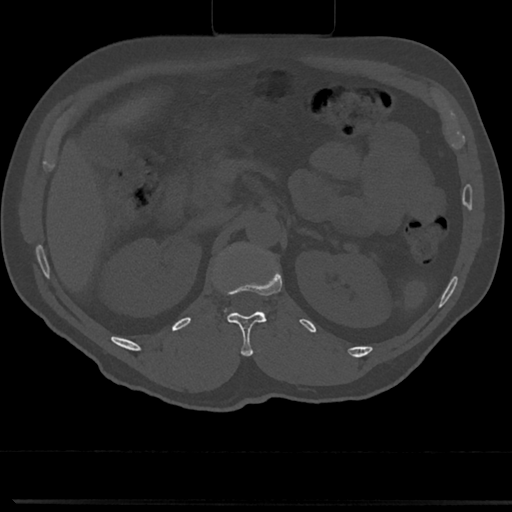
CT including the spine, one axial slice; reconstruction kernel Br40s/3; 120 kVp; bone window (W 1800 / L 400 HU); 512 × 512 image matrix. Patient: male, 61 years. From the clinical record (not read from this slice): primary cancer: prostate.
Outlined on this slice (semi-automatically segmented with operator editing):
- L1 vertebra: bounding box (x1, y1, x2, y2) in pixels: (212, 241, 274, 320)
- T12 vertebra: (225, 311, 267, 356)